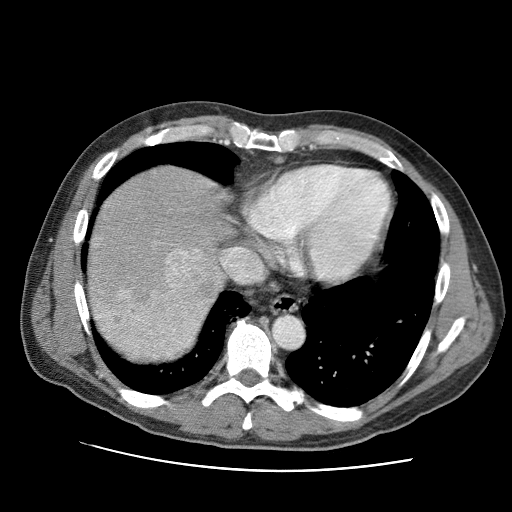
Contrast-enhanced abdominal CT (liver protocol), one axial slice. Slice 84 of 95 in the series (ordered by position). Reconstruction kernel STANDARD. One of 2 acquisitions stored at this slice position. Soft-tissue window (W 400 / L 40 HU). 512 × 512 image matrix. Case-level facts recorded for this patient, not image findings: diagnosis: hepatocellular carcinoma (patient treated with transarterial chemoembolisation; whether this scan precedes or follows treatment is not stated here); TNM stage (as recorded): Stage-IVA; Child-Pugh class: A.
Annotated regions visible in this slice (semi-automatic segmentation, software-assisted and operator-edited):
- liver parenchyma outside the tumour (the mass and vessels are separate outlines, so this box may not span the whole liver): bounding box [x1, y1, x2, y2] px = [88, 166, 234, 358]
- mass: [88, 197, 220, 363]
- liver vessels: [166, 260, 168, 263]